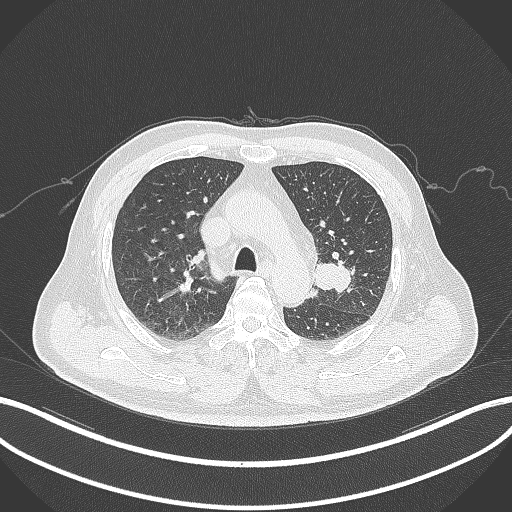
Chest CT, one axial slice; slice 210 of 286 in the series (ordered by position); lung window (W 1500 / L -600 HU); 1 mm slice thickness; 512 × 512 image matrix, field of view 400 × 400 mm. Male patient, age 67 years. Case-level facts recorded for this patient, not image findings: clinical TNM (as recorded): T2a N1 M0; histopathological grade: G3.
Outlined on this slice (bounding box drawn by a radiologist):
- lung tumour (recorded histology: adenocarcinoma): box from (x=310, y=261) to (x=354, y=294) px